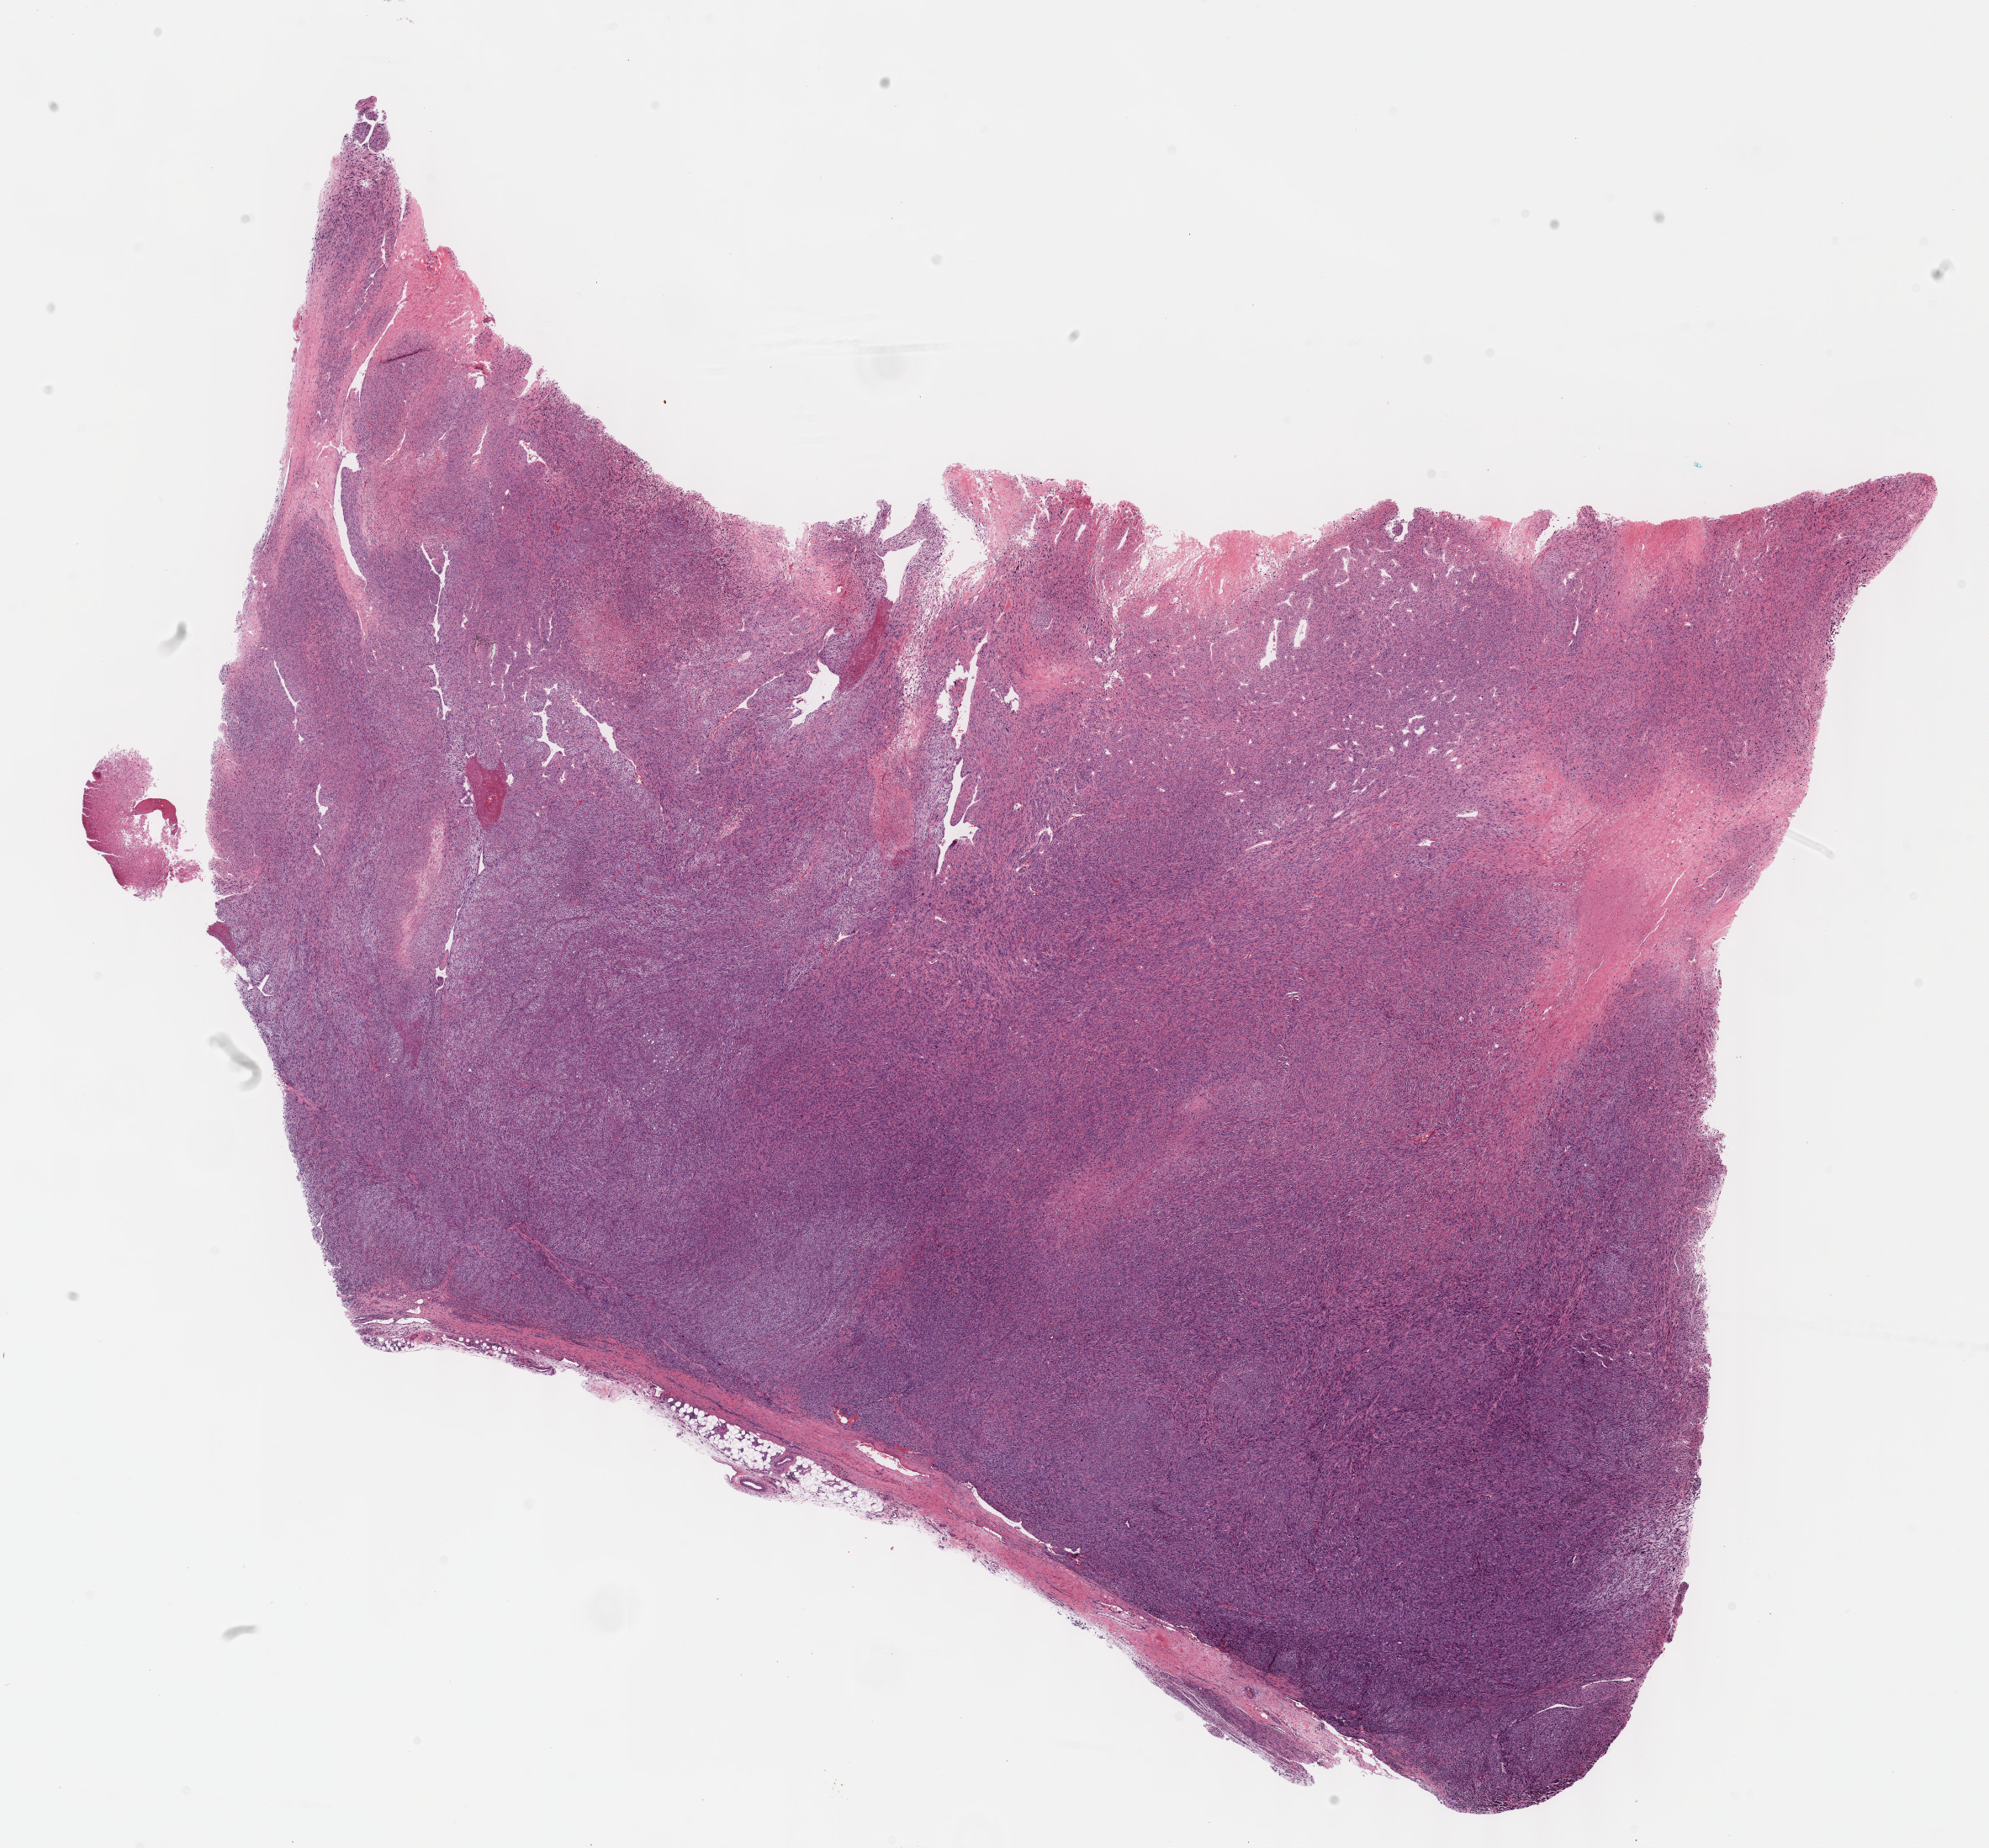
Digitized H&E tissue section (whole slide) — shown as a low-resolution overview of the whole scanned area (about 19.1 x 17.8 mm). Formalin-fixed paraffin-embedded (FFPE) diagnostic section. Sample: primary tumour, connective, subcutaneous and other soft tissues. Patient: female, age at initial diagnosis 68 years.
Pathologic diagnosis: Fibromyxosarcoma.